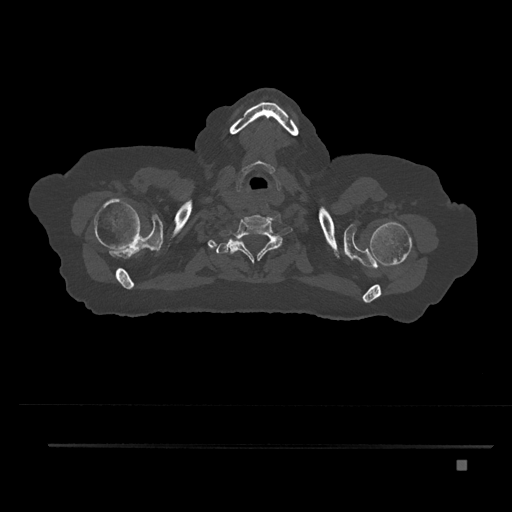
CT including the spine, one axial slice; slice 720 of 797 in the series (ordered by position); 120 kVp; bone window (W 1800 / L 400 HU); 0.5 mm slice thickness; 512 × 512 image matrix, field of view 437 × 437 mm. Female patient, age 76 years. From the clinical record (not read from this slice): primary cancer: lung.
Outlined on this slice (semi-automatic segmentation, software-assisted and operator-edited):
- T1 vertebra: bounding box <222,240,265,257> (left, top, right, bottom; pixels)